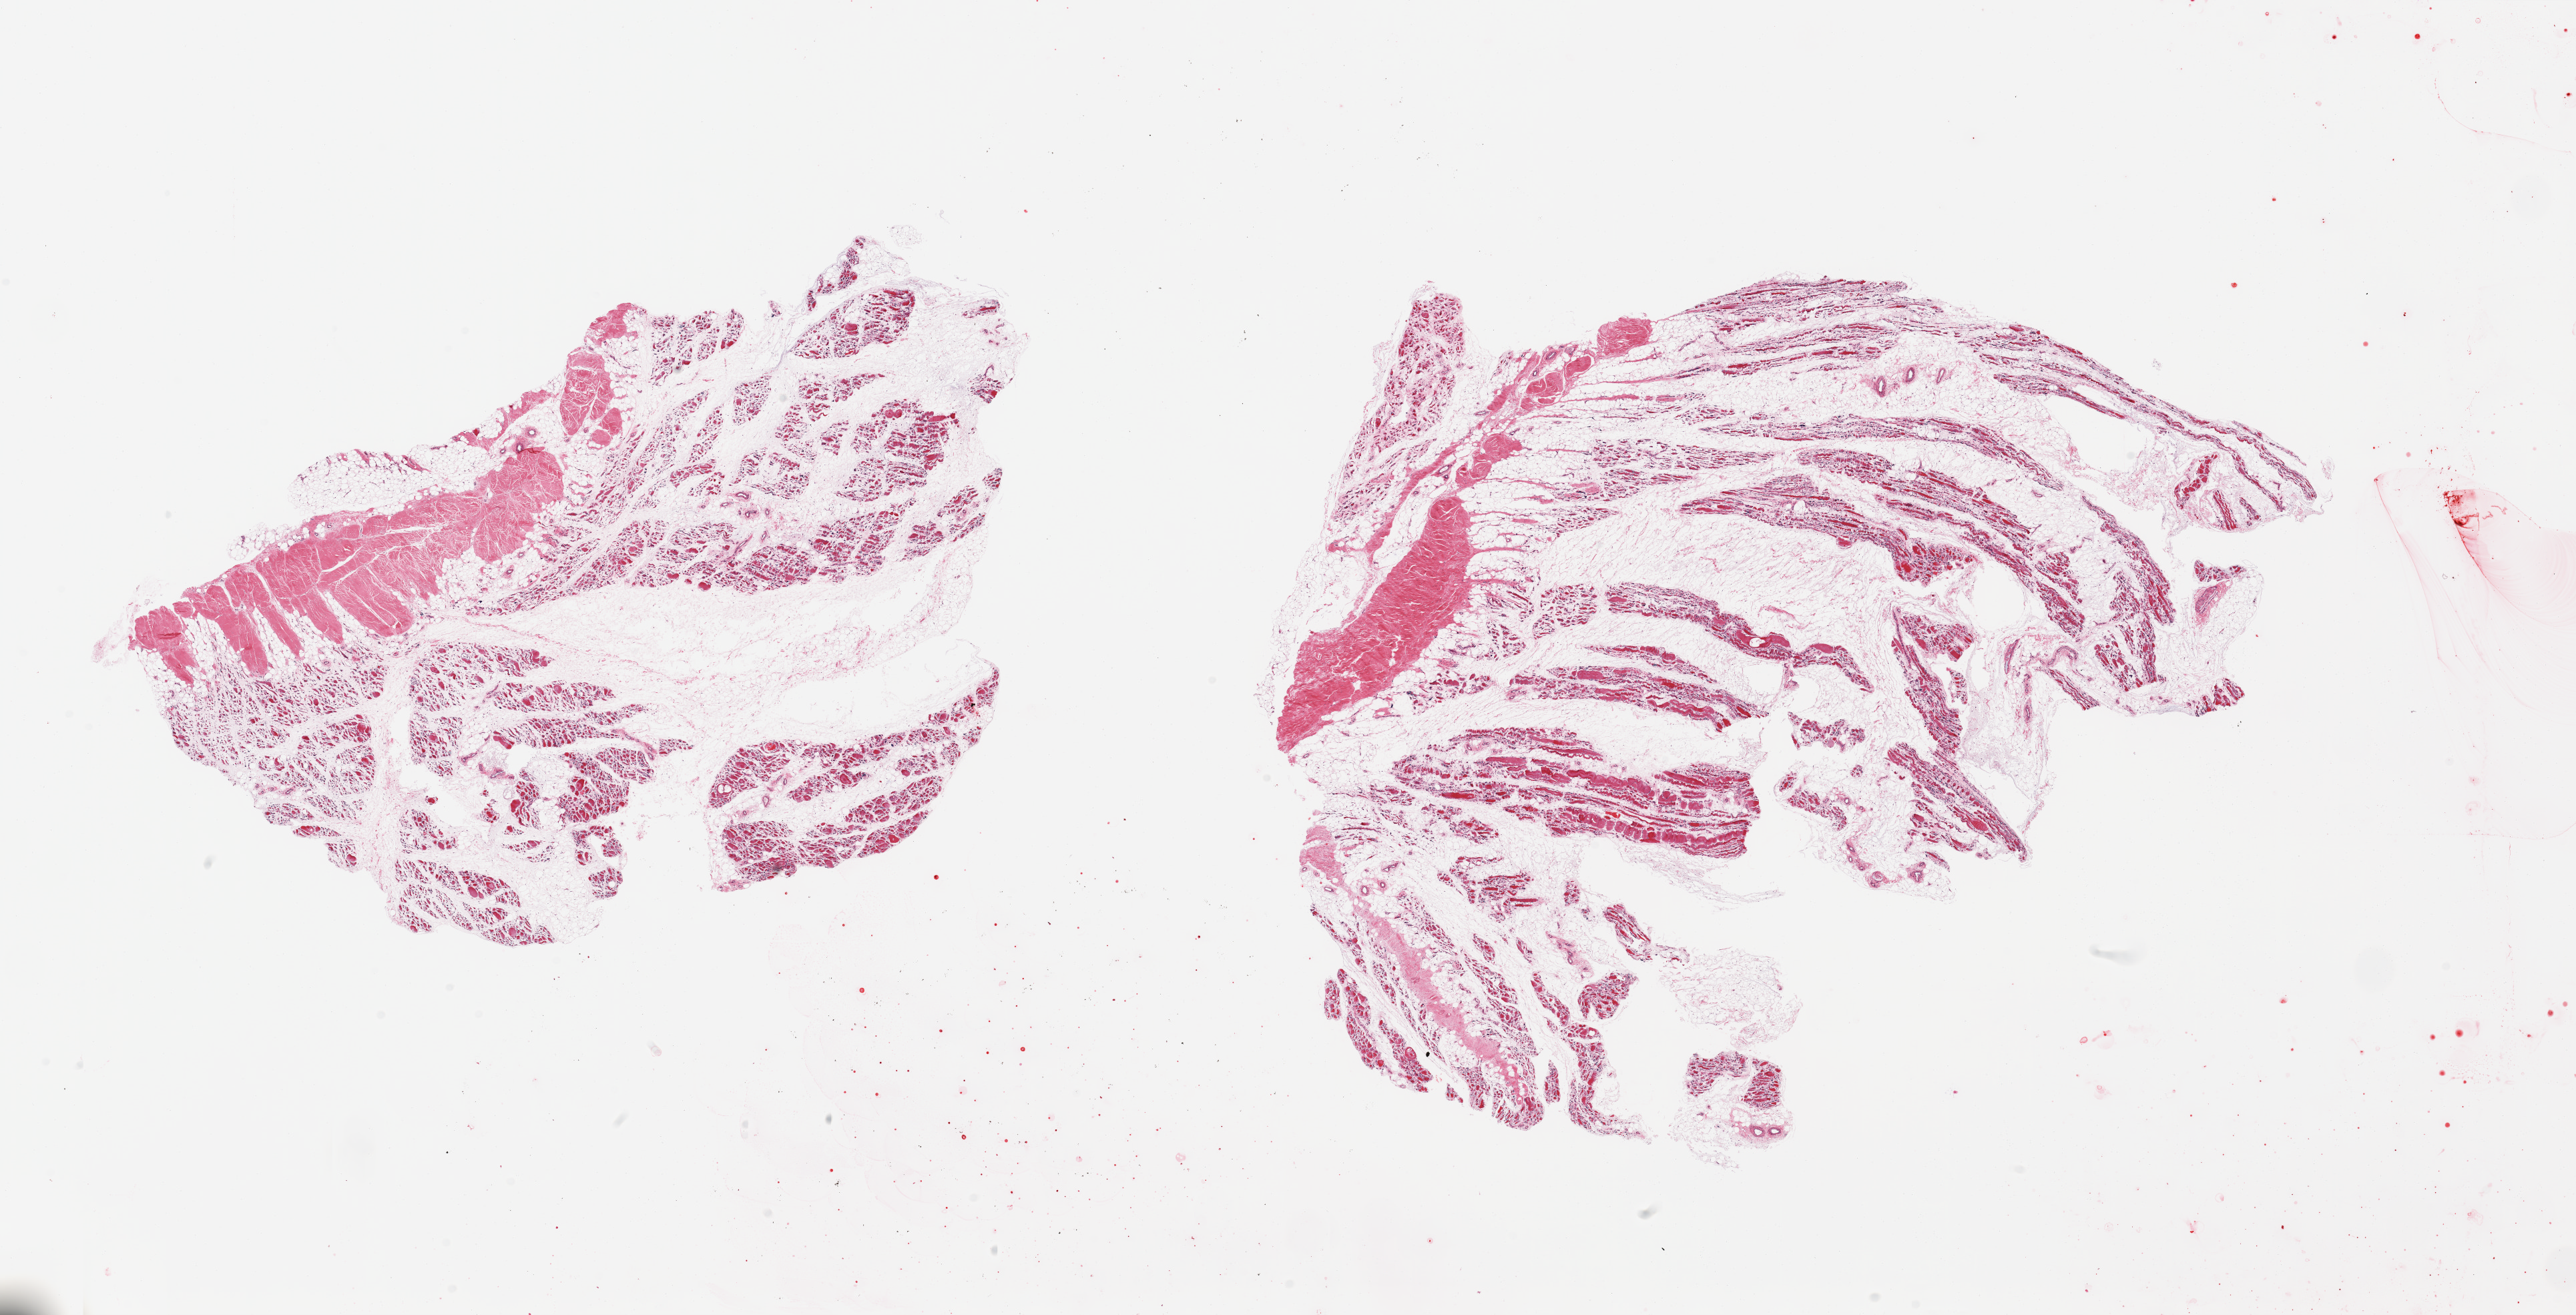
Digitized H&E-stained section, brightfield, whole scanned area (about 30.5 x 15.6 mm) shown as a low-resolution overview; PAXgene-fixed paraffin-embedded (PFPE) section; section of skeletal muscle (target tissue); tissue donor sample. Donor sex: female.
- review note (as recorded): 2 pieces; skeletal muscle with profound atrophy (c/w history of disuse), portion of tendon